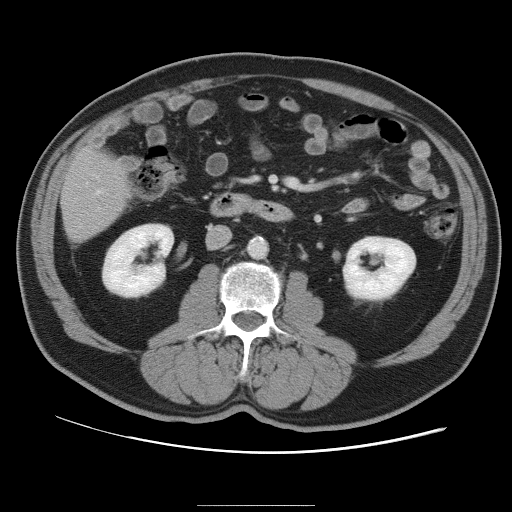
Contrast-enhanced abdominal CT, one axial slice; position 28 of 105 along the scan axis; 120 kVp; intravenous contrast given; soft-tissue window (W 400 / L 40 HU); 512 × 512 image matrix. Male patient, age 64 years. Case-level facts recorded for this patient, not image findings: diagnosis: colorectal cancer liver metastases, imaged before liver resection.
Structures marked on this image (expert manual segmentation):
- hepatic veins: bounding box <97,191,101,193> (left, top, right, bottom; pixels)
- liver: <64,152,129,240>
- planned liver remnant (the part of the liver to remain after resection): <64,151,129,230>